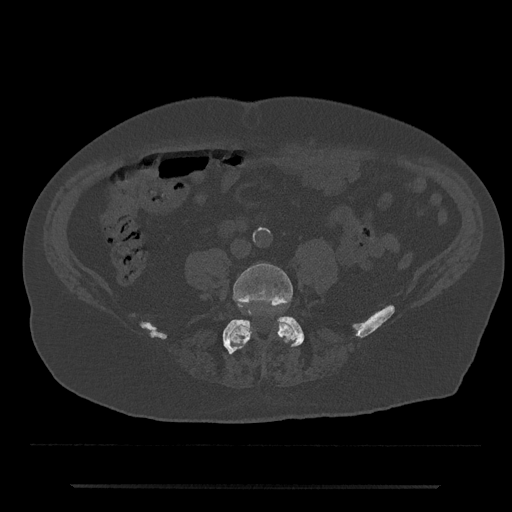
CT including the spine, one axial slice; position 323 of 797 along the scan axis; 120 kVp; bone window (W 1800 / L 400 HU); 512 × 512 image matrix, field of view 434 × 434 mm. Patient: male, 80 years. From the clinical record (not read from this slice): primary cancer: prostate; vertebrae with lytic lesions (as recorded): L1, T11.
Annotated regions visible in this slice (semi-automatic segmentation, software-assisted and operator-edited):
- L4 vertebra: bounding box <228,263,297,349> (left, top, right, bottom; pixels)
- L5 vertebra: <222,317,304,354>